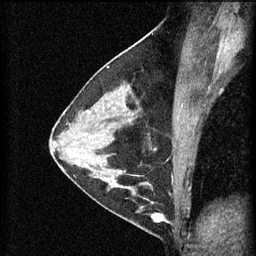
Breast MRI (dynamic contrast-enhanced), one sagittal slice. Position 33 of 60 along the scan axis. 3 images stored at this slice position (order not interpretable as contrast timing). 1.5 T. TE 4.2 ms, TR 11 ms. 256 × 256 image matrix, field of view 180 × 180 mm. Patient: female, 29 years.
Structures marked on this image (semi-automatically segmented with operator editing):
- analysis volume of interest (the breast-tissue region the enhancement analysis was run in; not a lesion): bounding box <105,172,171,227> (left, top, right, bottom; pixels)
- tumour enhancement mask (voxels above the 70 % enhancement threshold inside the analysis volume of interest): <109,172,170,223>